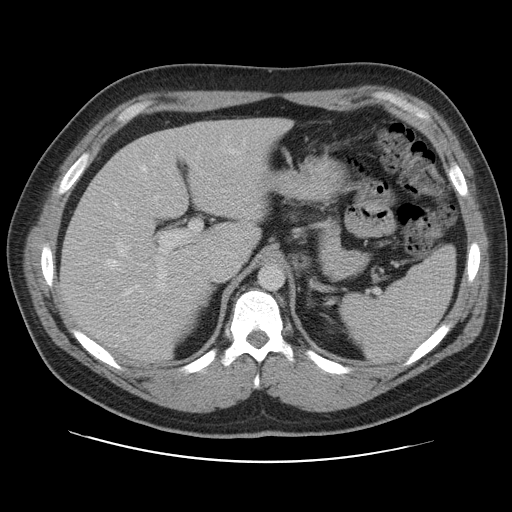
Contrast-enhanced abdominal CT, one axial slice; slice 75 of 109 in the series (ordered by position); 120 kVp; intravenous contrast given; soft-tissue window (W 400 / L 40 HU); 5 mm slice thickness; 512 × 512 image matrix, field of view 402 × 402 mm. Male patient, age 35 years. From the clinical record (not read from this slice): diagnosis: colorectal cancer liver metastases, imaged before liver resection; multiple liver metastases: yes; largest metastasis: 2.8 cm; chemotherapy before resection: yes.
Structures marked on this image (outlined manually by an expert reader):
- hepatic veins: bounding box [x1, y1, x2, y2] px = [105, 148, 240, 296]
- liver: [61, 119, 287, 362]
- planned liver remnant (the part of the liver to remain after resection): [61, 119, 281, 359]
- portal vein (with intrahepatic branches): [117, 160, 203, 299]